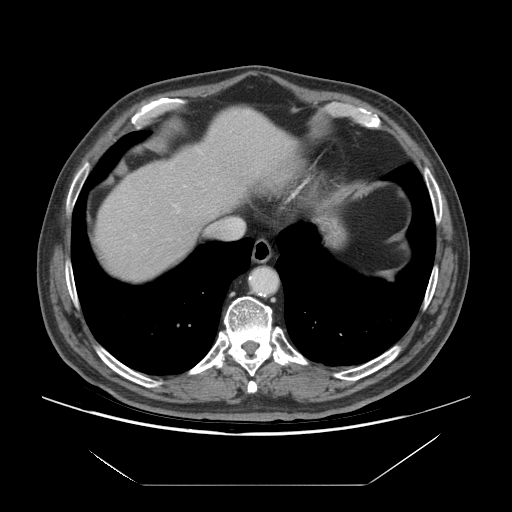
Contrast-enhanced abdominal CT (liver protocol), one axial slice. Slice 62 of 75 in the series (ordered by position). Reconstruction kernel STANDARD. 140 kVp. Soft-tissue window (W 400 / L 40 HU). 2.5 mm slice thickness. 512 × 512 image matrix, field of view 420 × 420 mm. Case-level facts recorded for this patient, not image findings: diagnosis: hepatocellular carcinoma (patient treated with transarterial chemoembolisation; whether this scan precedes or follows treatment is not stated here); TNM stage (as recorded): Stage-I; Child-Pugh class: A.
Outlined on this slice (semi-automatic segmentation, software-assisted and operator-edited):
- liver parenchyma outside the tumour (the mass and vessels are separate outlines, so this box may not span the whole liver): bounding box [x1, y1, x2, y2] px = [96, 108, 300, 280]